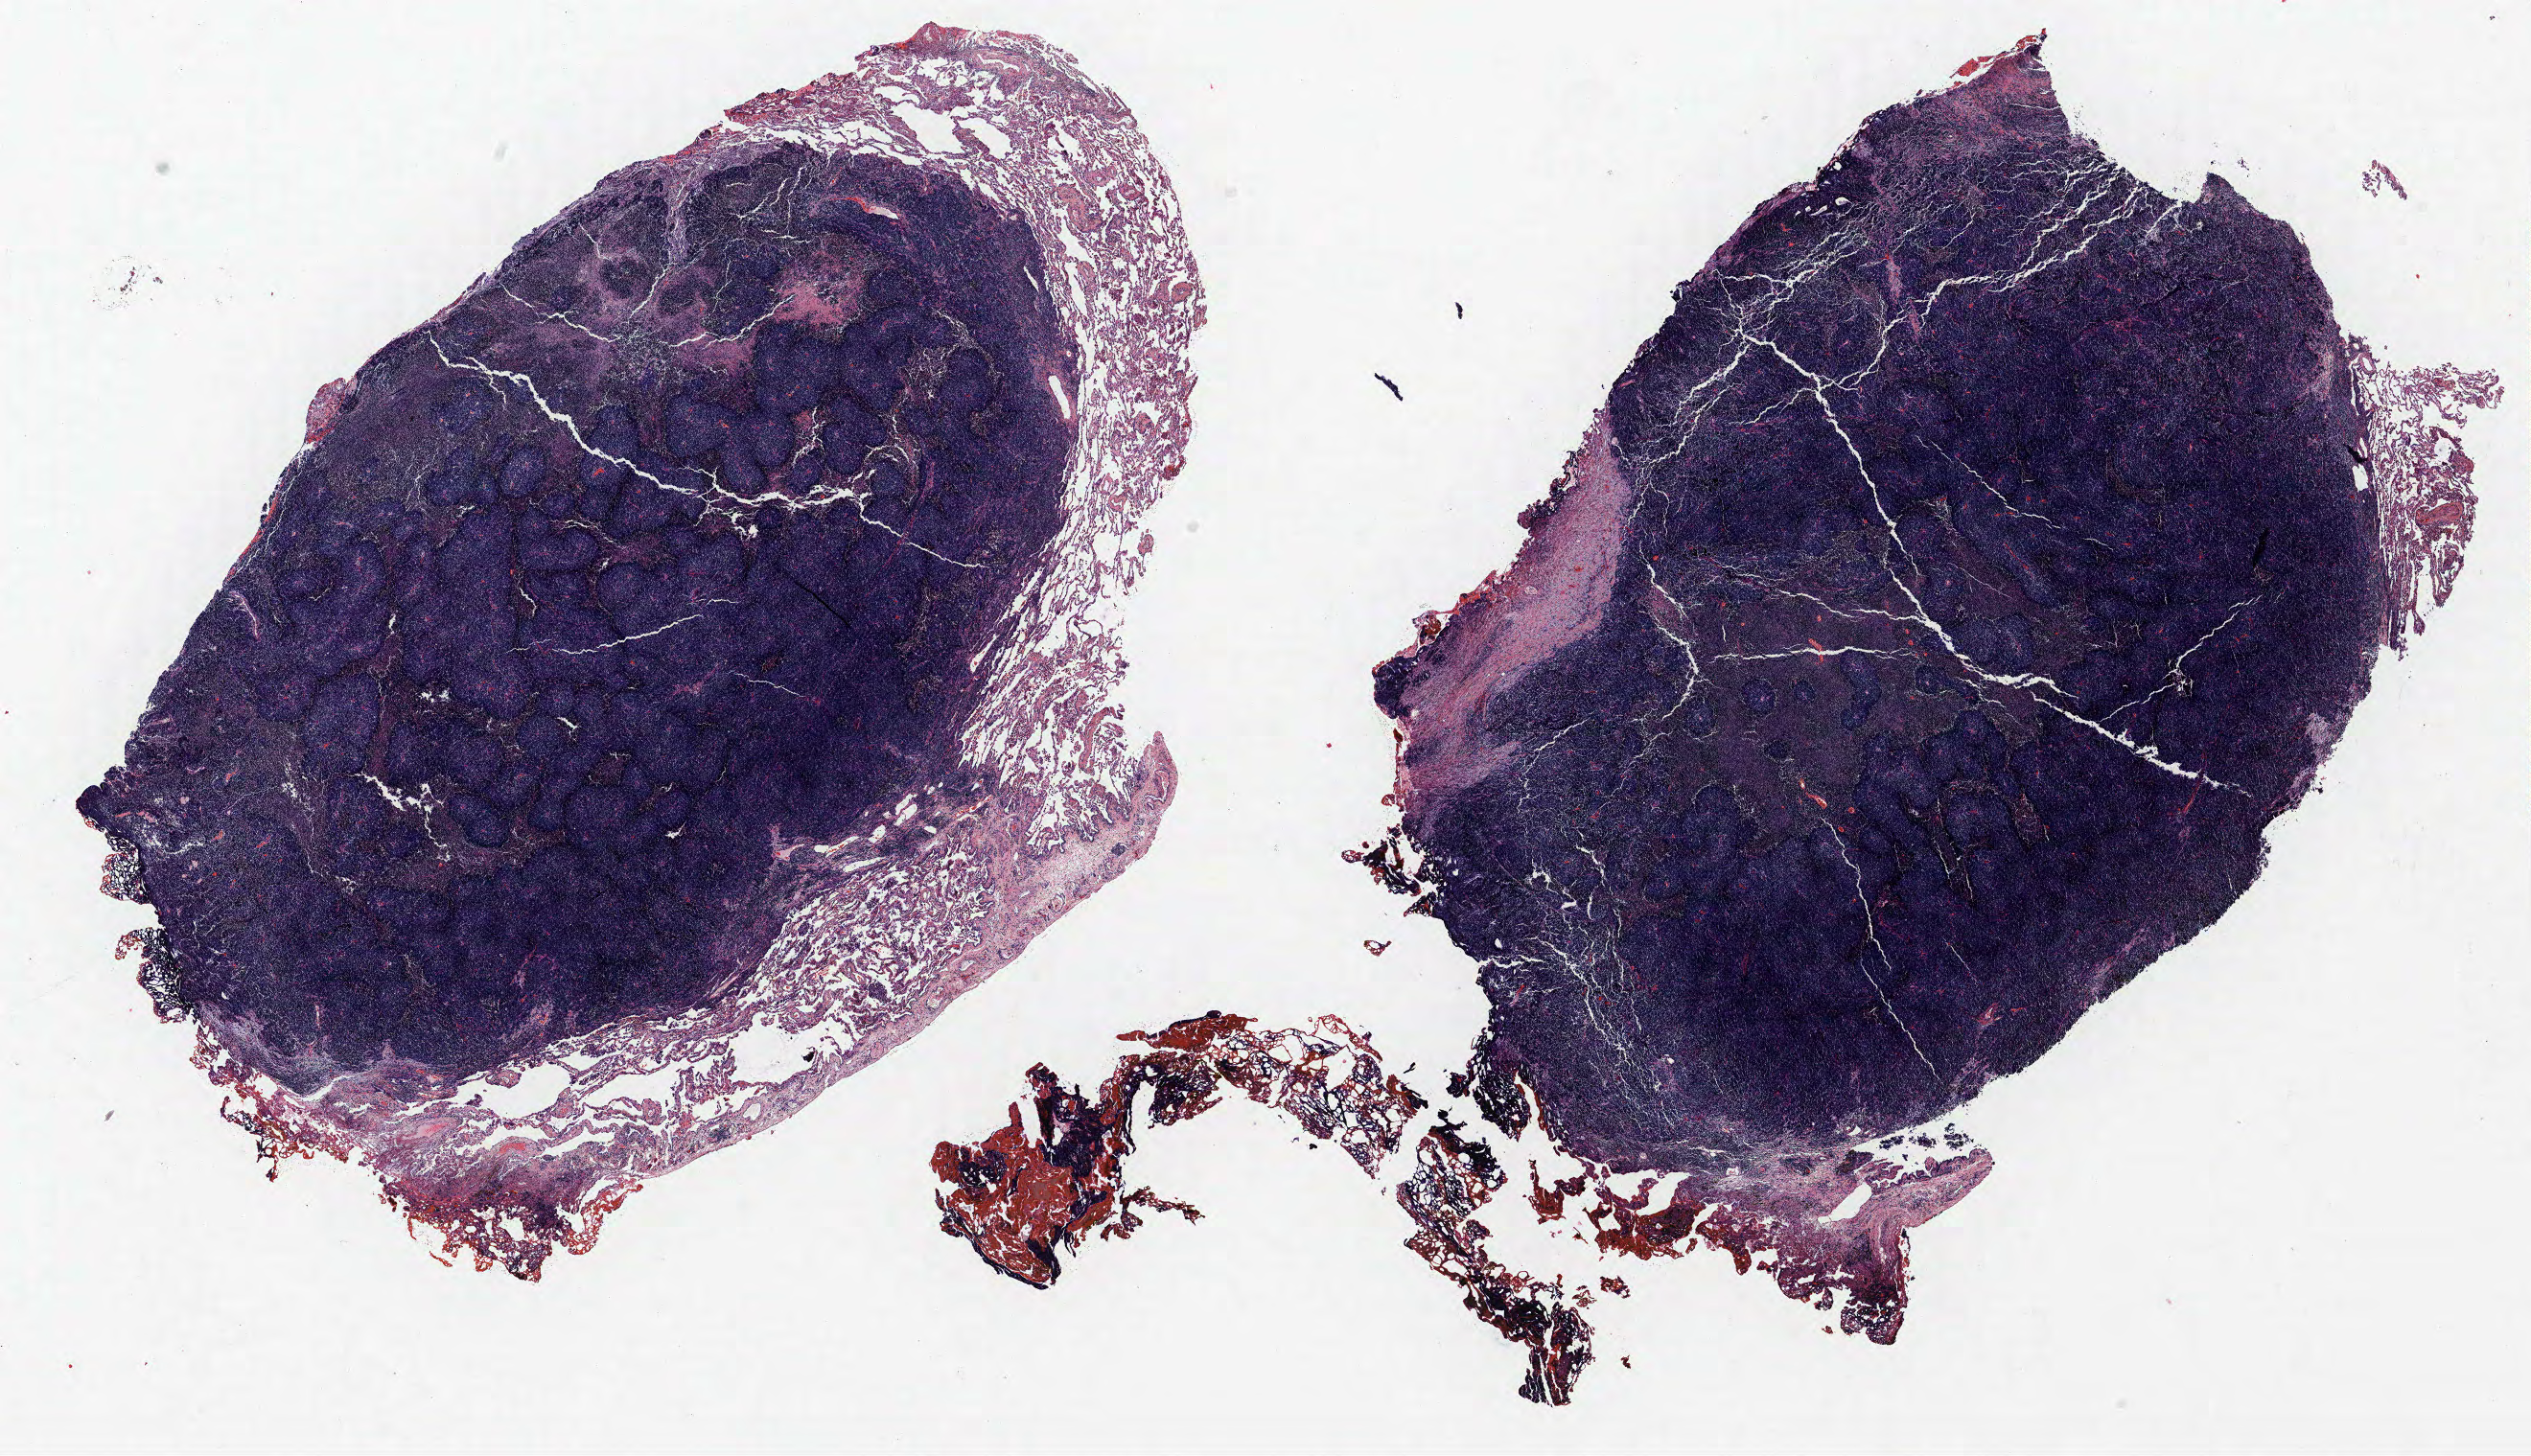
H&E whole-slide image — whole scanned area (about 21.1 x 12.2 mm, slide scanned at 40x) shown as a low-resolution overview, formalin-fixed paraffin-embedded (FFPE) section, lung. Male, age 59 at enrolment. Current smoker at enrolment.
Participant's lung-cancer diagnosis: Oat cell carcinoma (ICD-O-3 8042/3).